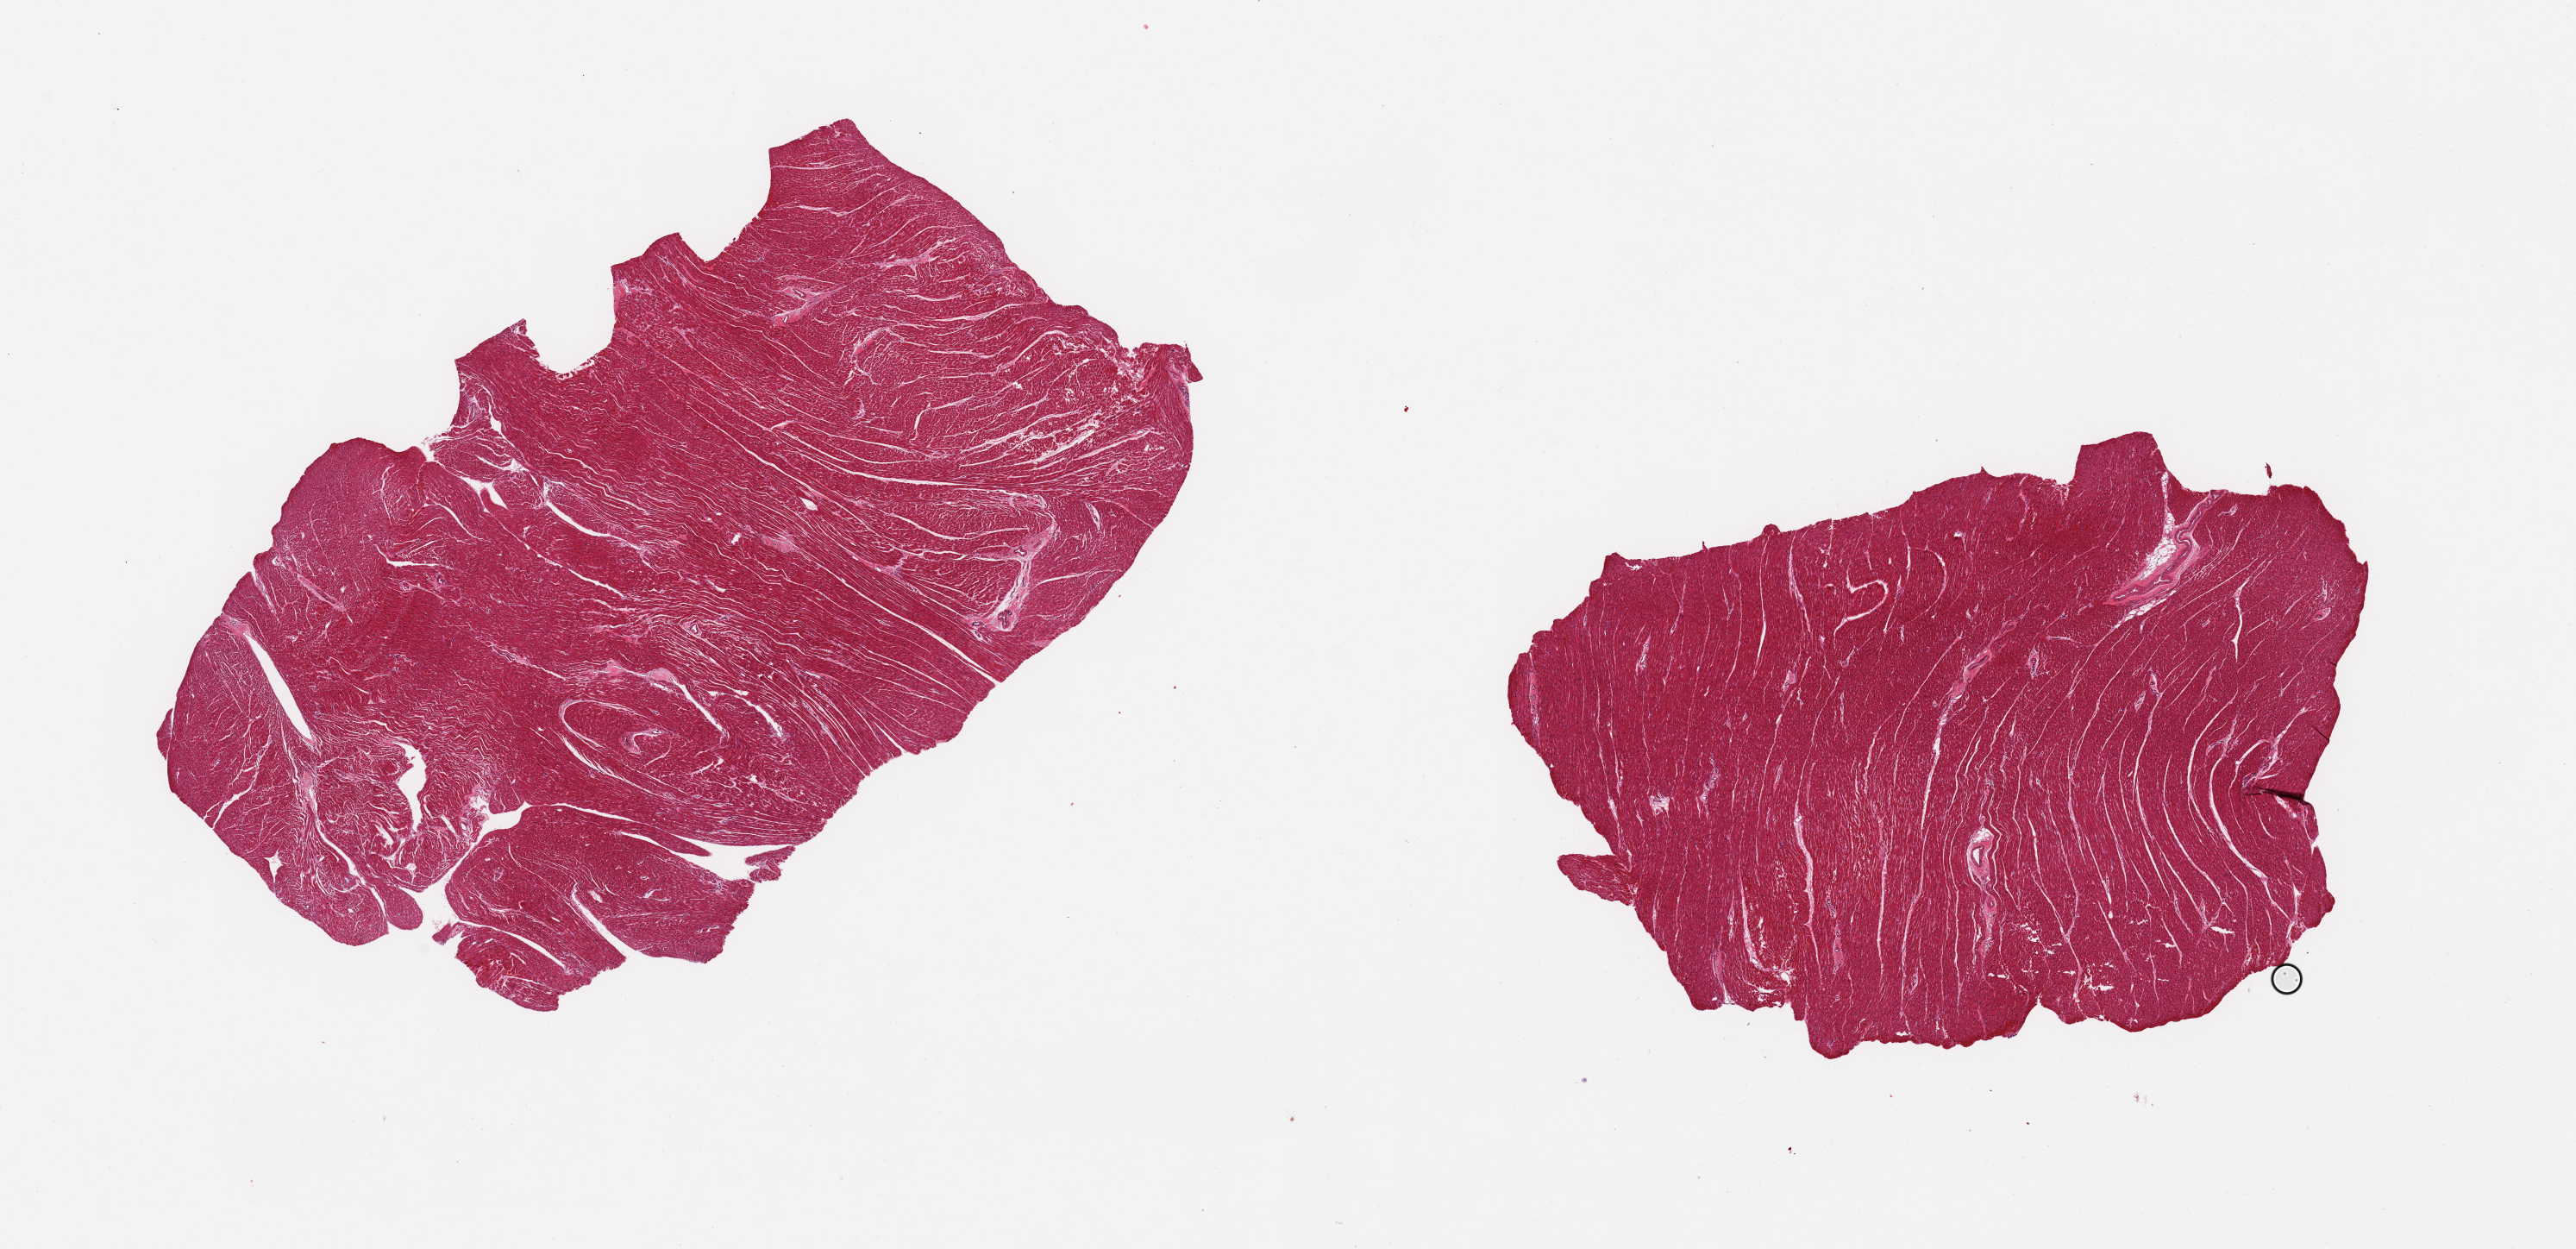
Hematoxylin and eosin (H&E) whole-slide image, whole scanned area (about 23.6 x 11.5 mm) shown as a low-resolution overview; PAXgene-fixed paraffin-embedded (PFPE) section; sampled site (target tissue): heart; tissue donor sample. Donor: female.
- pathologist's review note for this sample: 2 pieces, 8x5 & 8x6mm